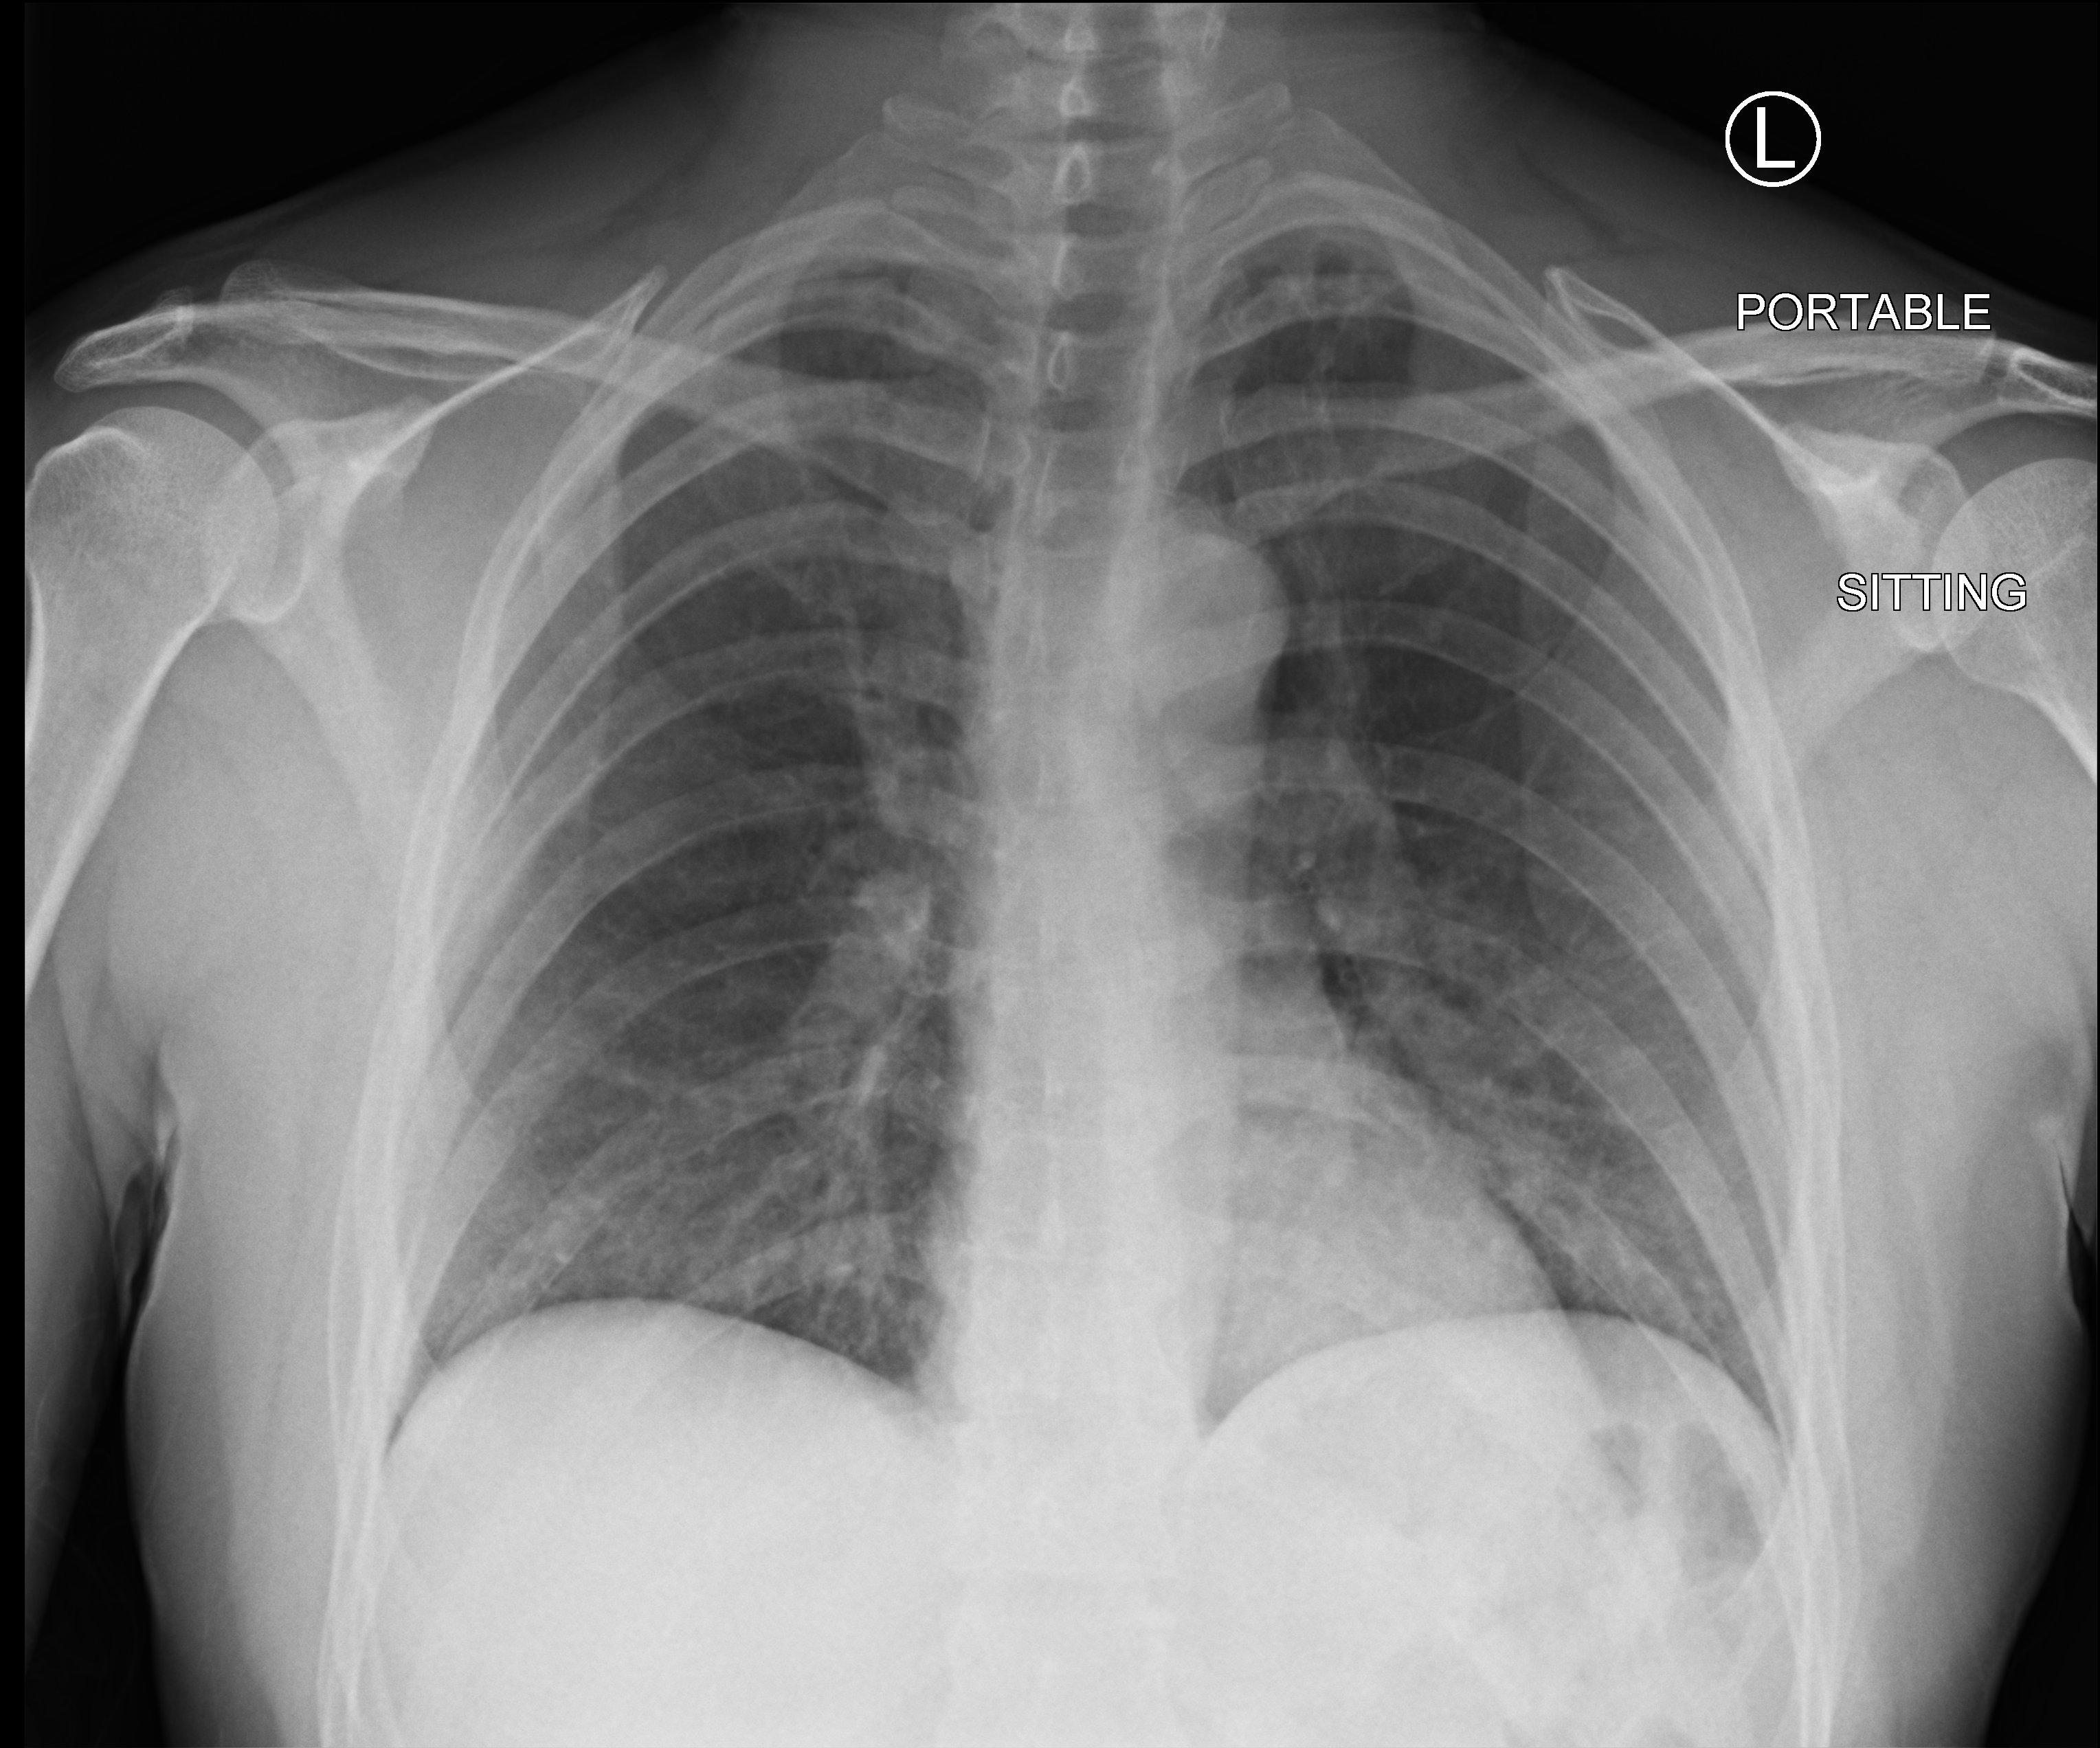
Bedside chest radiograph (computed radiography). Patient hospitalised with COVID-19; male, aged 18–59 years.
Hospital-stay facts (about this admission, not read from this image; timing relative to this image not recorded): smoking status (admission record): never; admitted to intensive care during this hospital stay: no; mechanically ventilated during this hospital stay: no.